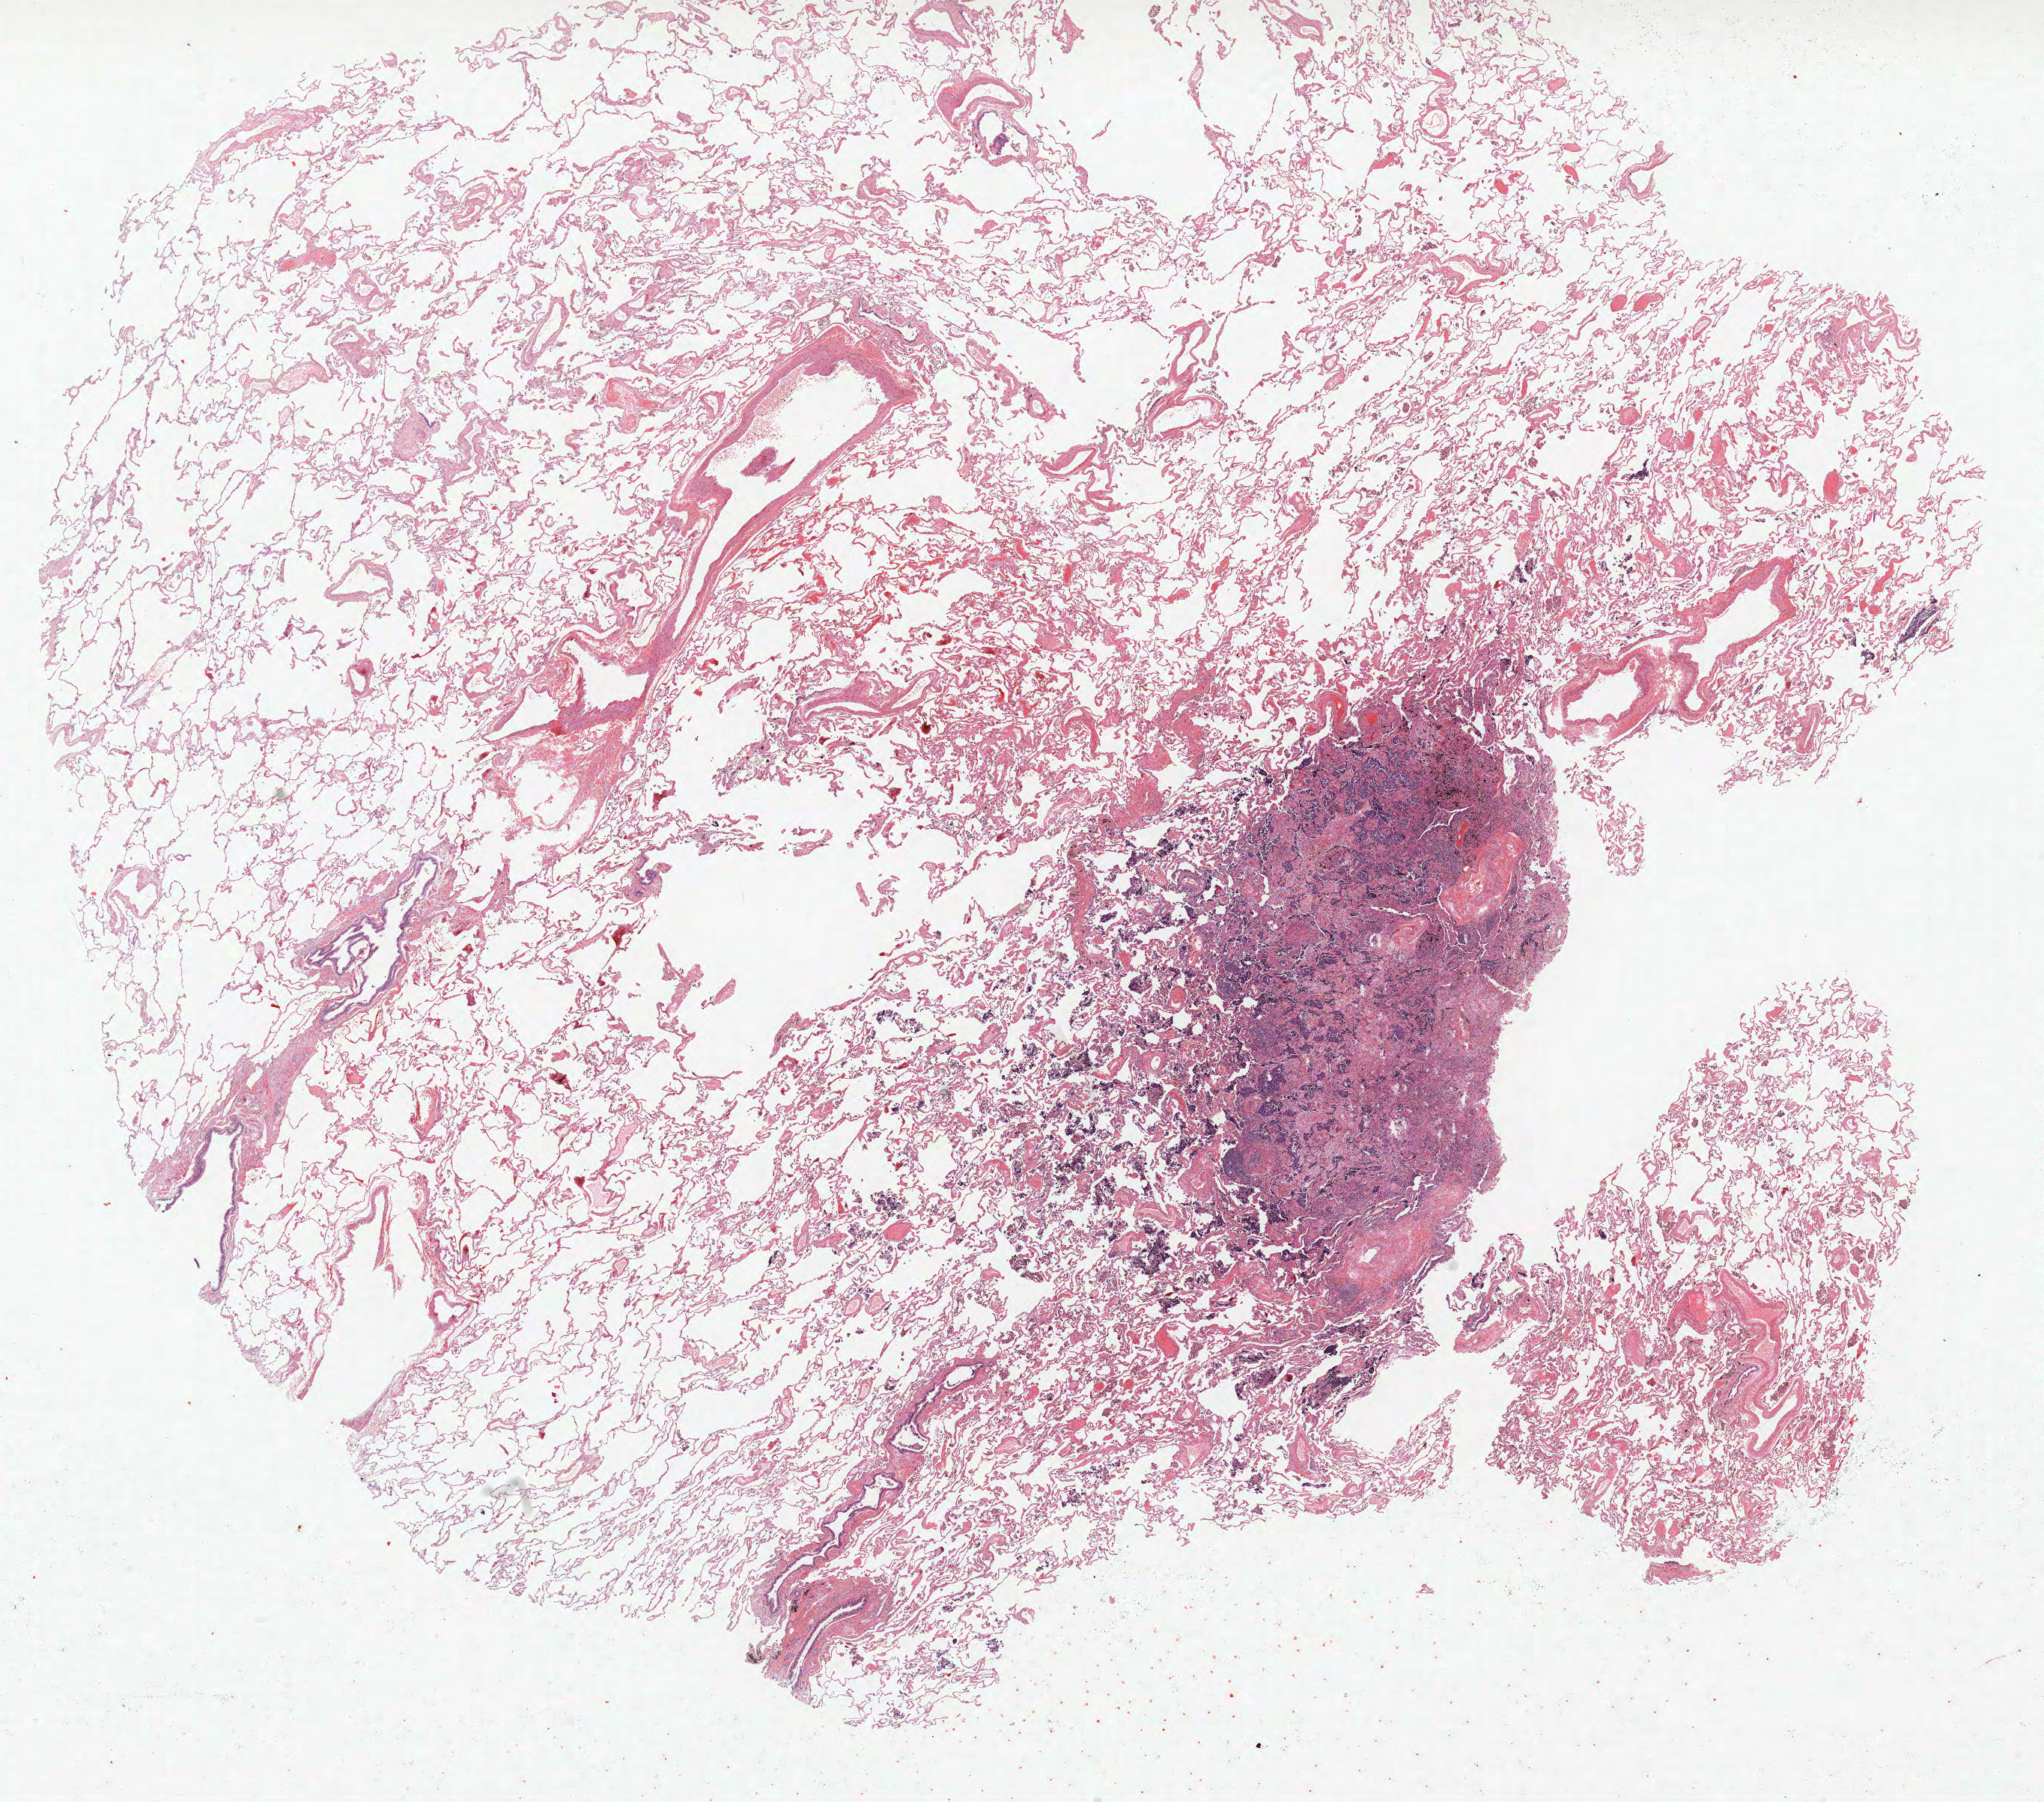
H&E whole-slide image, shown as a low-resolution overview of the whole scanned area (about 21.8 x 19.3 mm, from a 40x scan); FFPE section; lung. Male, age 70 at enrolment.
- primary tumour location (clinical record): right upper lobe
- participant's lung-cancer diagnosis: Small cell carcinoma, NOS
- stage (AJCC 6th edition): IA
- tumour size (pathology): 11 mm